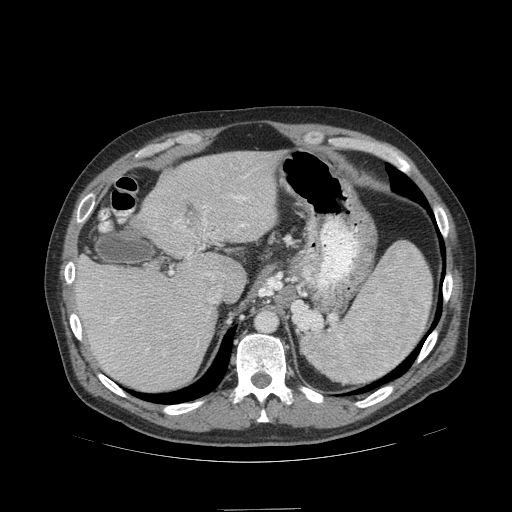
Contrast-enhanced abdominal CT (liver protocol), one axial slice; position 75 of 99 along the scan axis; 140 kVp; soft-tissue window (W 400 / L 40 HU); 512 × 512 image matrix. Case-level facts recorded for this patient, not image findings: diagnosis: hepatocellular carcinoma (patient treated with transarterial chemoembolisation; whether this scan precedes or follows treatment is not stated here); TNM stage (as recorded): Stage-I; Child-Pugh class: A; tumour size: 3.6 cm.
Structures marked on this image (semi-automatically segmented with operator editing):
- liver parenchyma outside the tumour (the mass and vessels are separate outlines, so this box may not span the whole liver): bounding box [x1, y1, x2, y2] px = [72, 150, 282, 390]
- liver vessels: [72, 174, 249, 357]